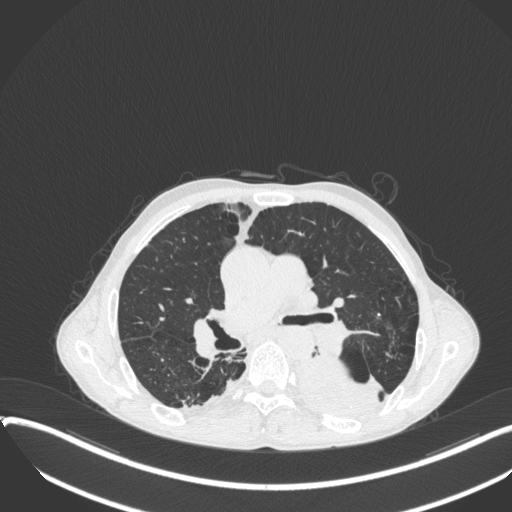
Chest CT, one axial slice; slice 222 of 400 in the series (ordered by position); lung window (W 1500 / L -600 HU); 512 × 512 image matrix, field of view 400 × 400 mm. Patient: male, 57 years. Case-level facts recorded for this patient, not image findings: clinical TNM (as recorded): T4 N0 M0.
Annotated regions visible in this slice (bounding box drawn by a radiologist):
- lung tumour (recorded histology: squamous cell carcinoma): bounding box <288,344,390,425> (left, top, right, bottom; pixels)